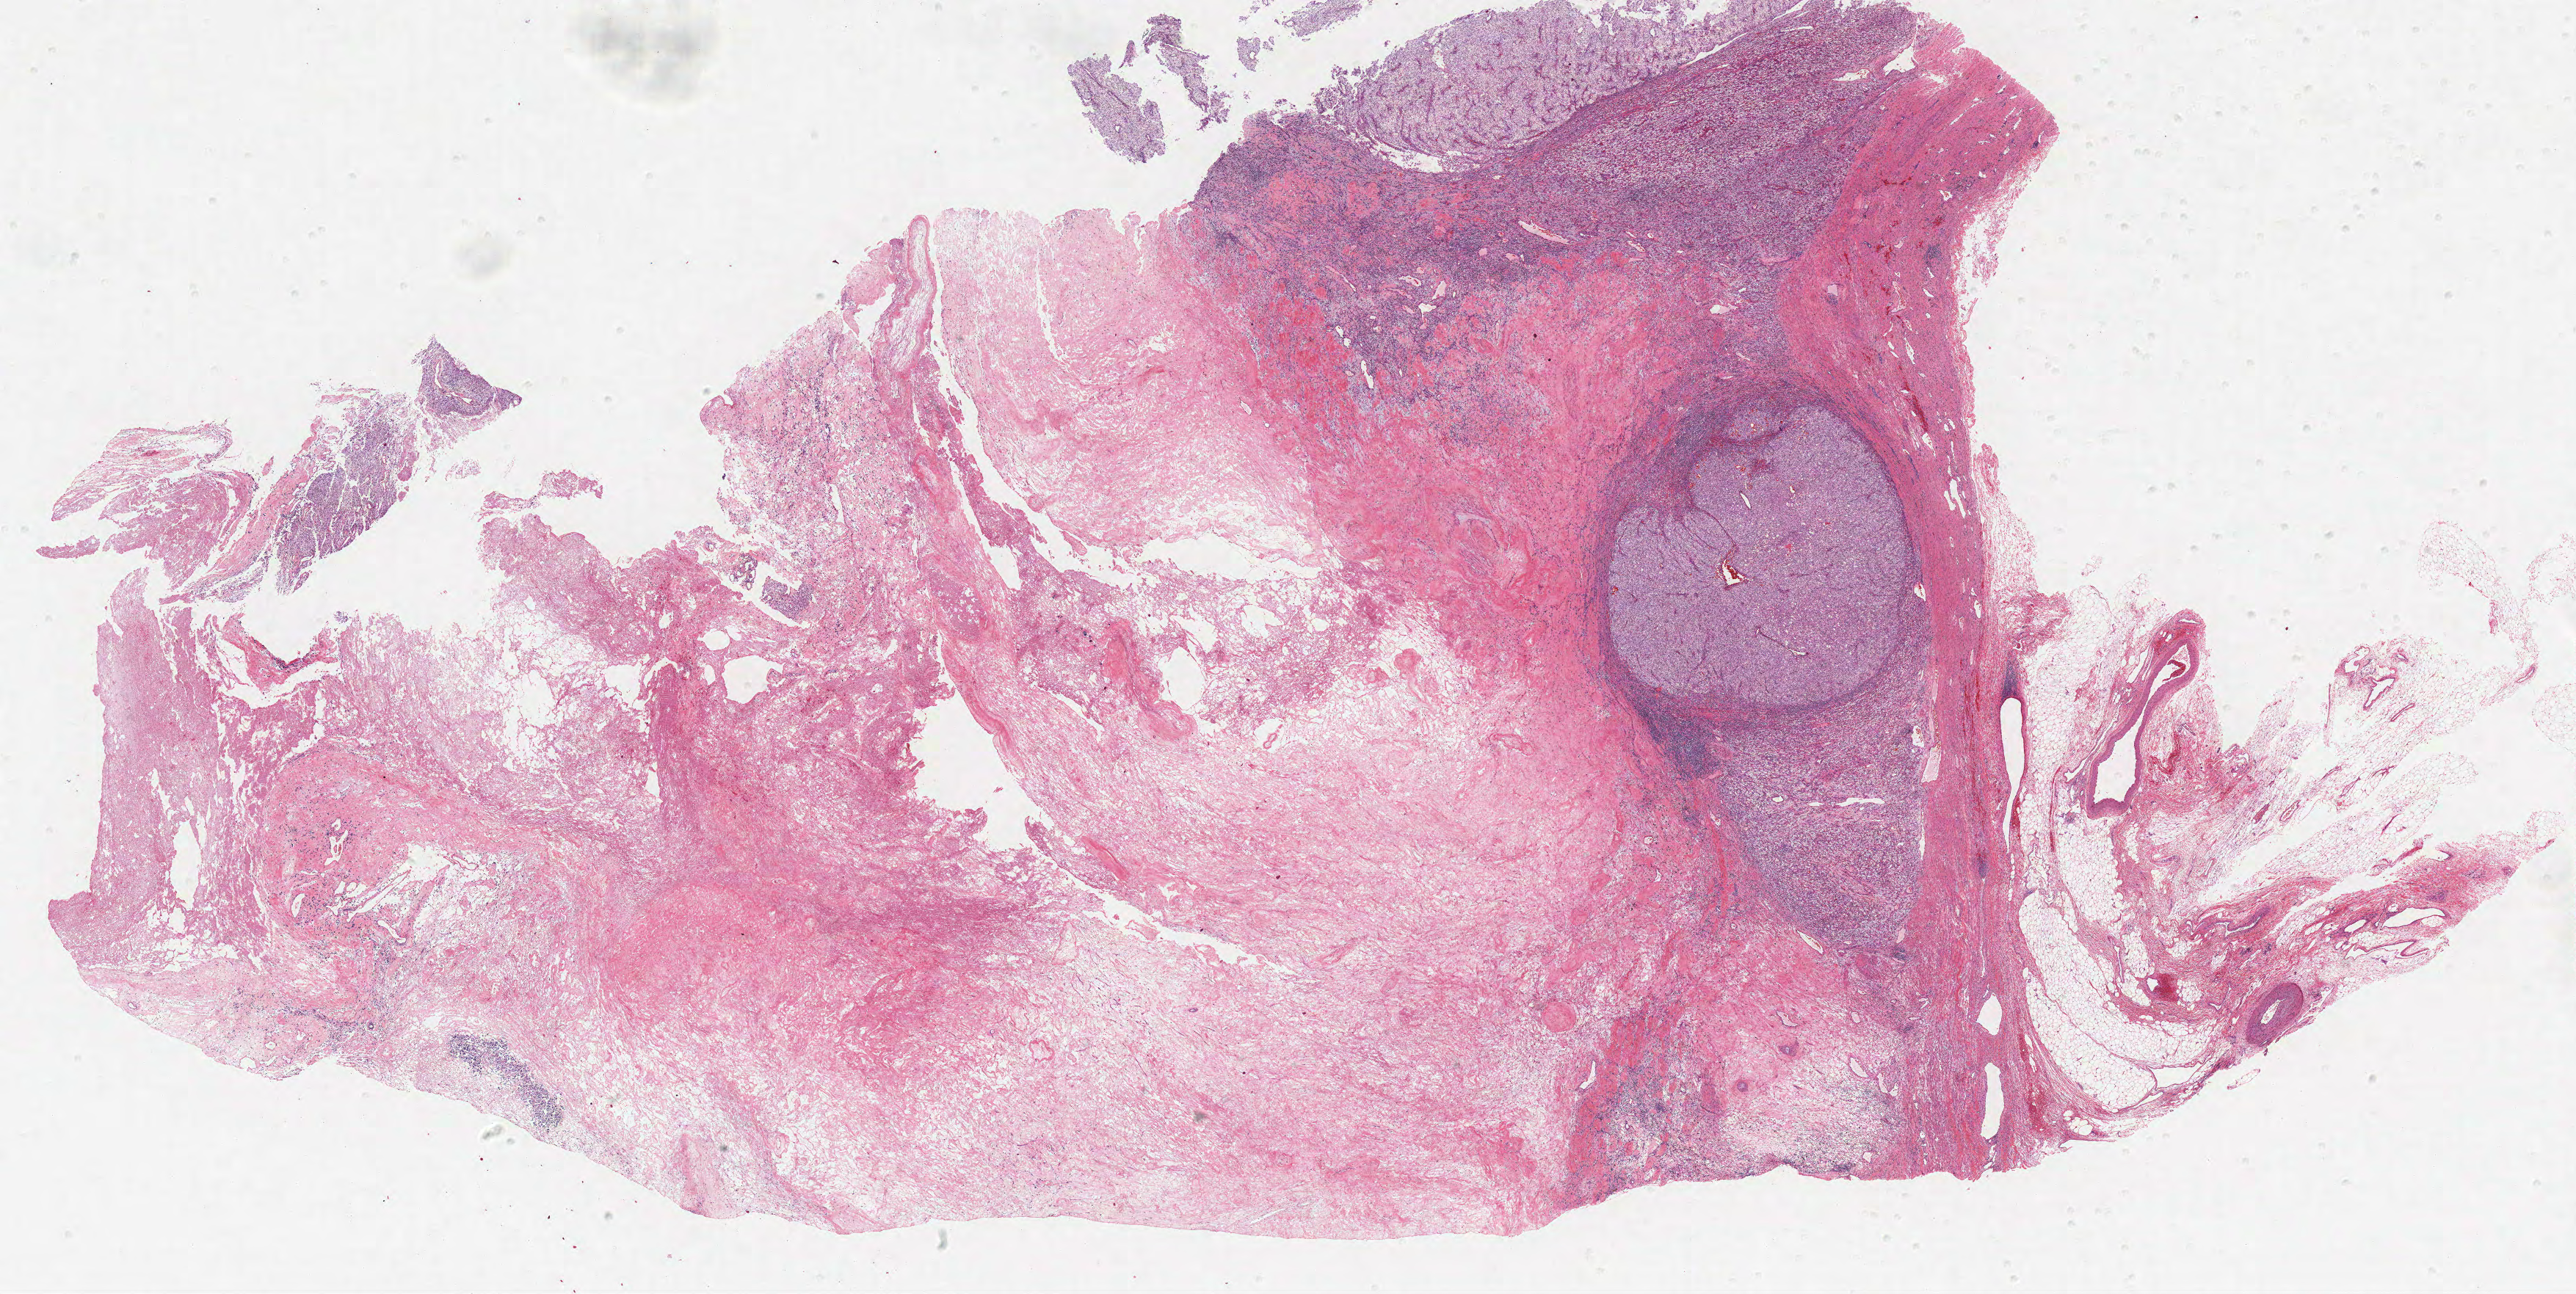
Whole-slide histology image, Hematoxylin and eosin (H&E) stained, shown as a low-resolution overview of the whole scanned area (about 28.1 x 14.1 mm). Formalin-fixed paraffin-embedded (FFPE) diagnostic section. Sample: primary tumour, kidney. Male, age 44 years at initial diagnosis. Histologic grade: G4 (undifferentiated).
- pathologic diagnosis: Clear cell adenocarcinoma, NOS
- AJCC pathologic stage: II
- laterality: right